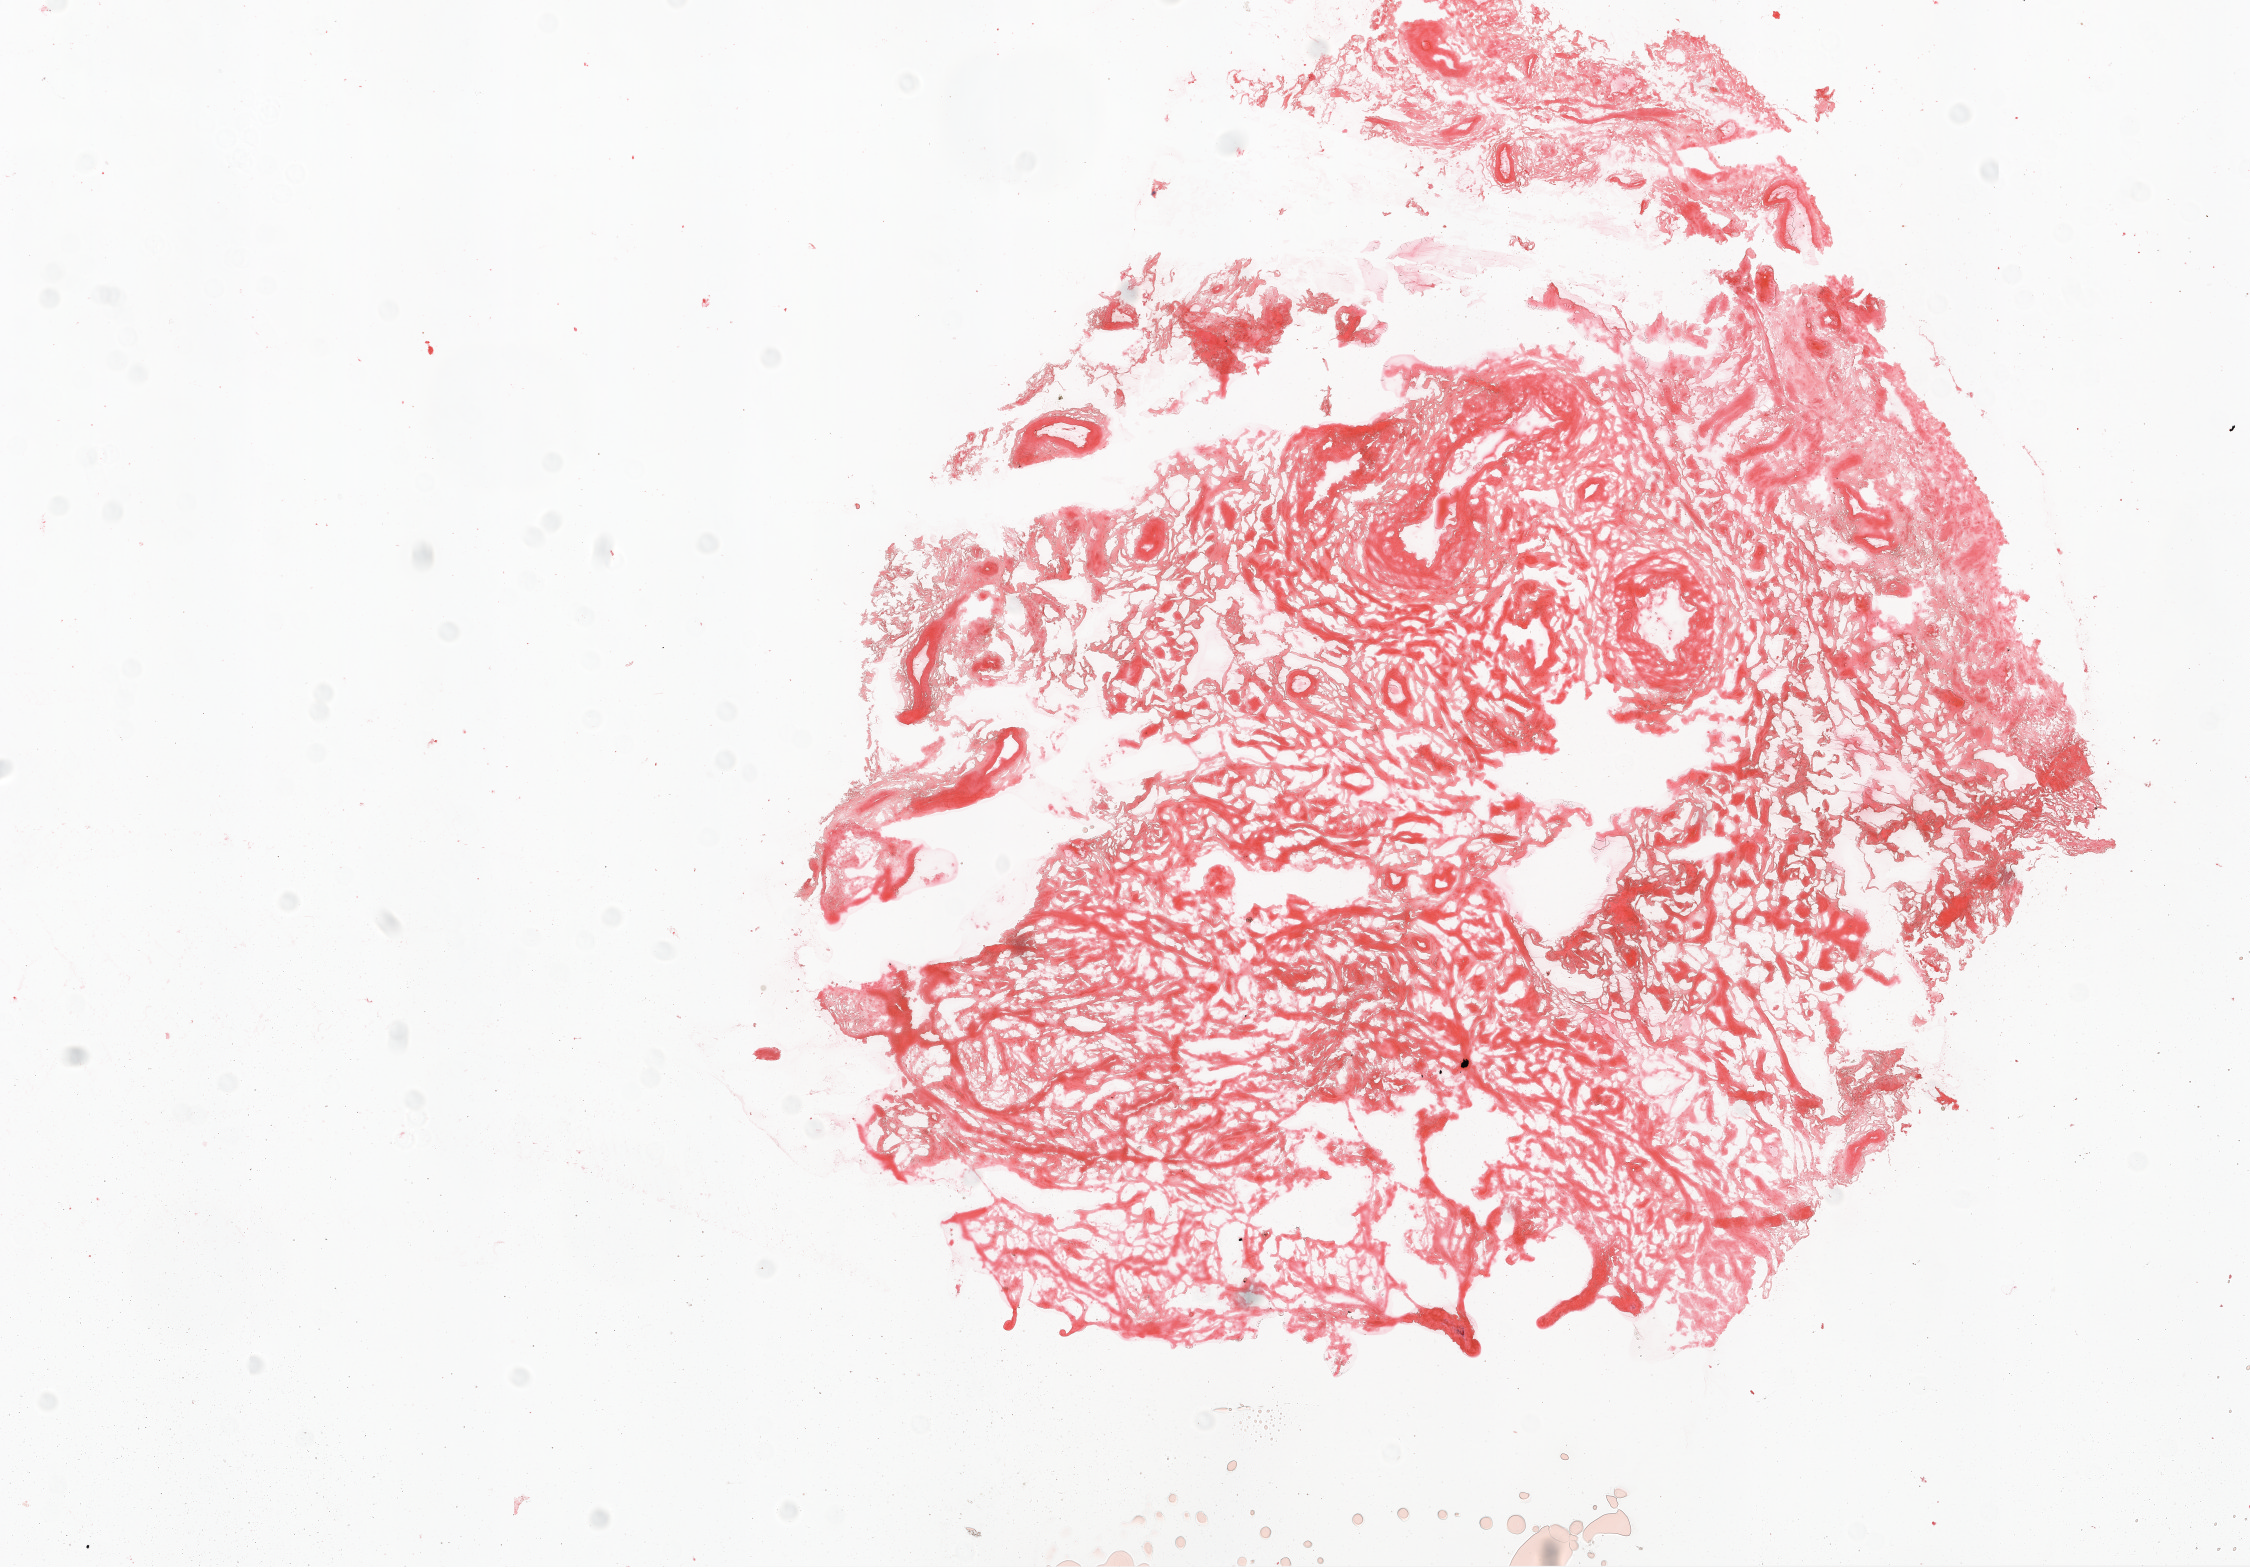
H&E whole-slide image — whole scanned area (about 9.0 x 6.3 mm, acquisition: 20x scan) shown as a low-resolution overview, frozen section, solid tissue normal (non-tumour tissue) sample from the ovary. Female patient; age at initial diagnosis 60 years.
- this section: solid tissue normal (non-tumour) sample from the same patient
- patient diagnosis: Serous cystadenocarcinoma, NOS